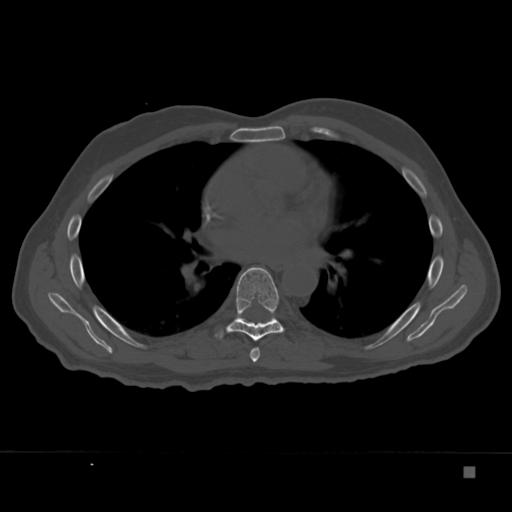
CT including the spine, one axial slice. Position 224 of 332 along the scan axis. 120 kVp. Bone window (W 1800 / L 400 HU). 1.5 mm slice thickness. 512 × 512 image matrix, field of view 389 × 389 mm. Male patient, age 72 years. From the clinical record (not read from this slice): primary cancer: skeletal.
Outlined on this slice (semi-automatically segmented with operator editing):
- T6 vertebra: bounding box (x1, y1, x2, y2) in pixels: (250, 348, 260, 362)
- T7 vertebra: (216, 267, 284, 341)